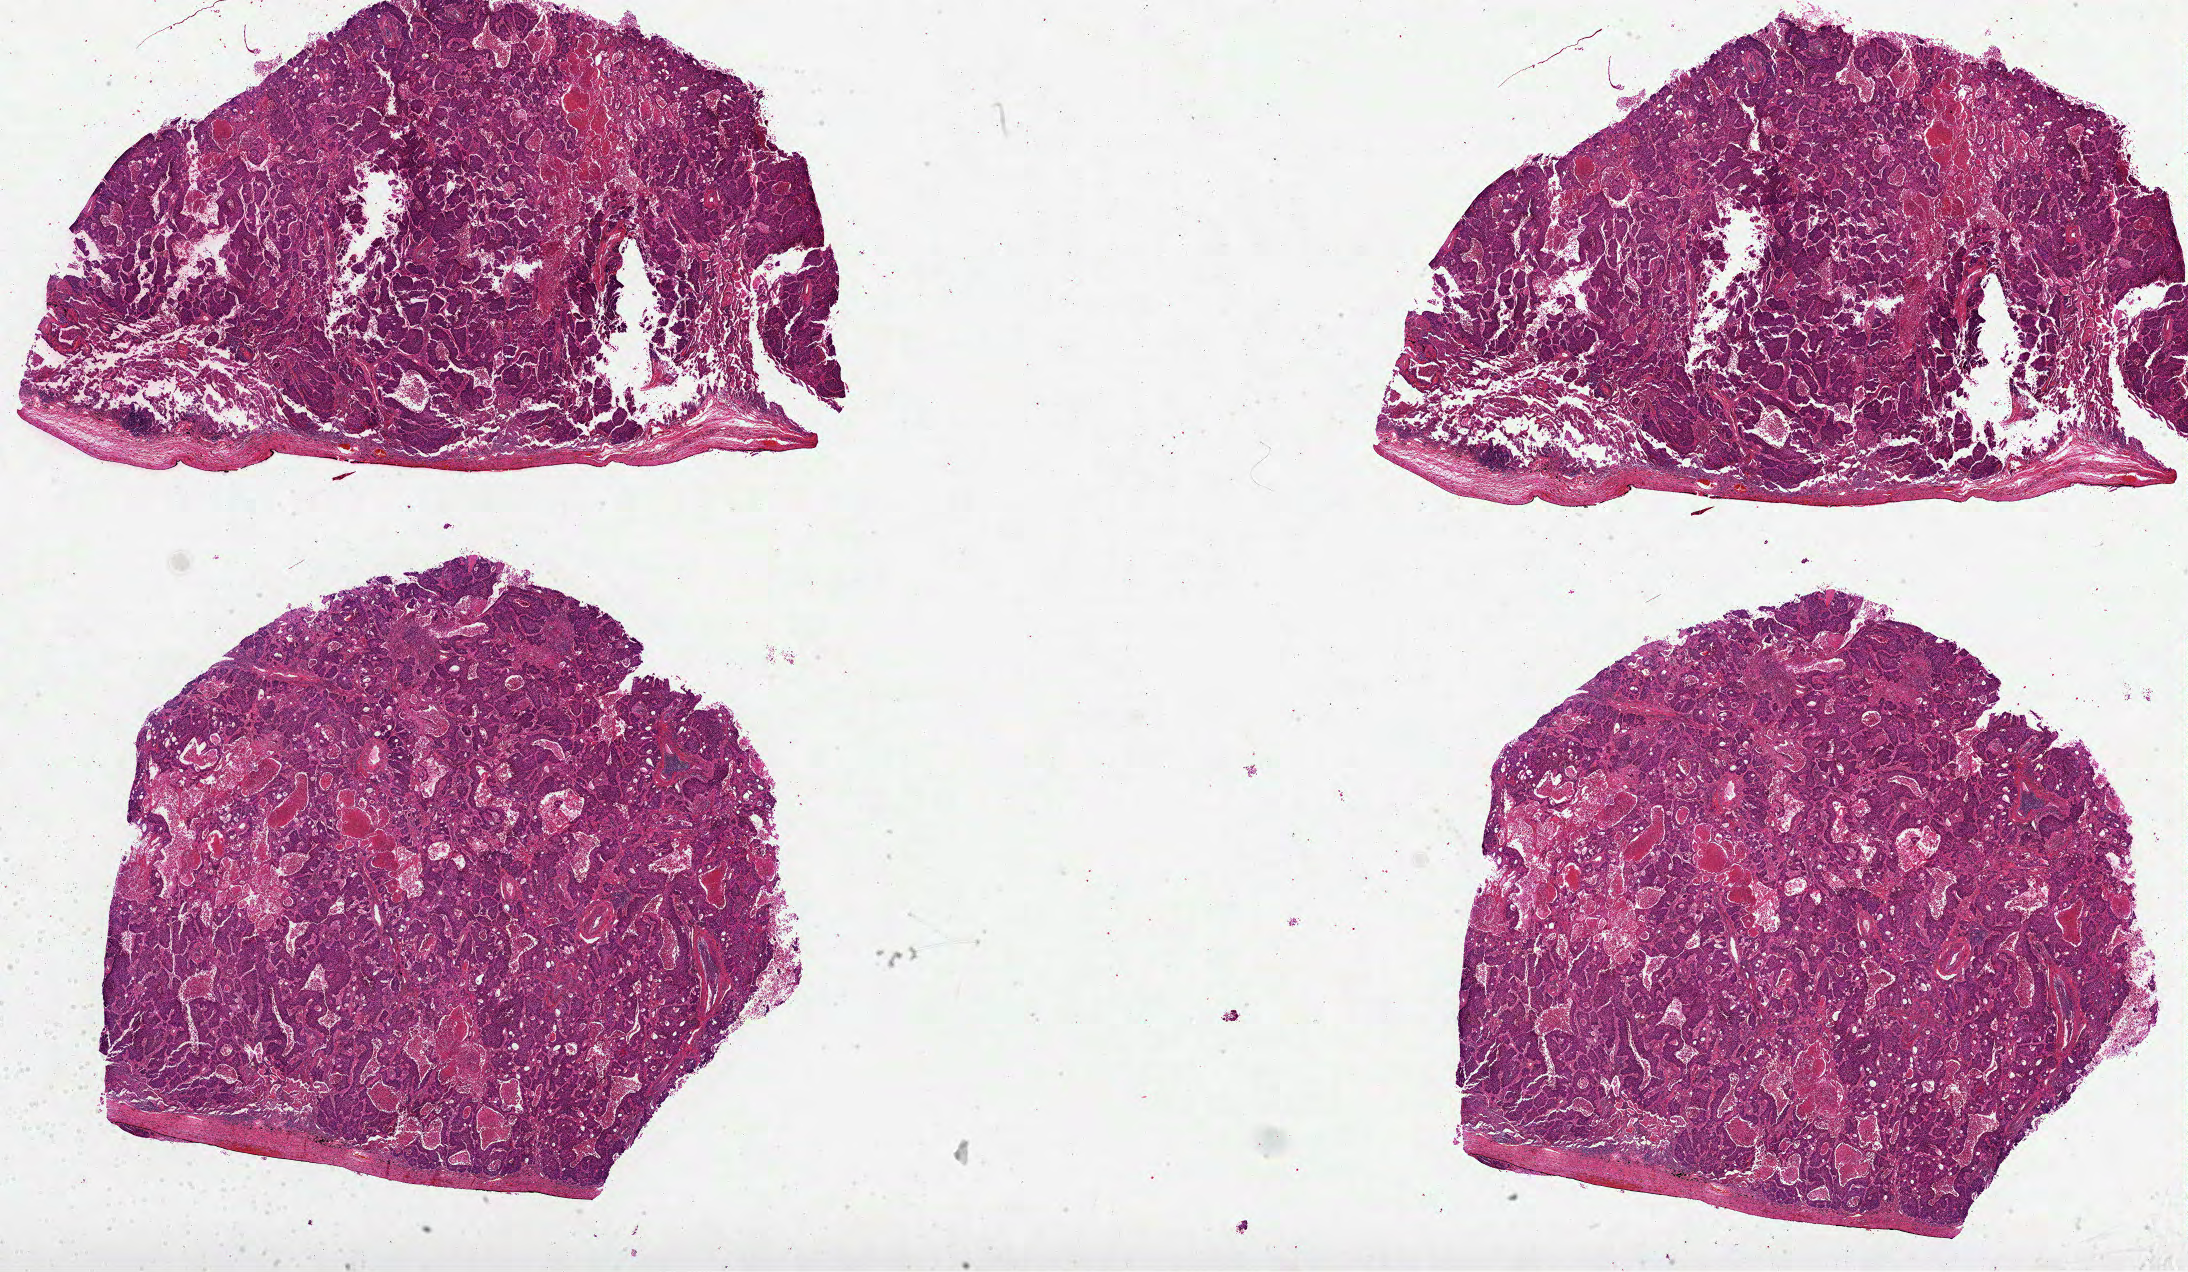
Digitized Hematoxylin and eosin (H&E) stained tissue section (whole slide) — a low-resolution overview of the entire scanned area, about 35.3 x 20.5 mm. Formalin-fixed paraffin-embedded (FFPE) diagnostic section. Primary tumour sample from the lung. Male patient; age at initial diagnosis 68 years.
* AJCC pathologic stage: IB (5th edition)
* laterality: right
* diagnosis: Squamous cell carcinoma, NOS (lower lobe, lung)
* TNM: T2 N0 M0